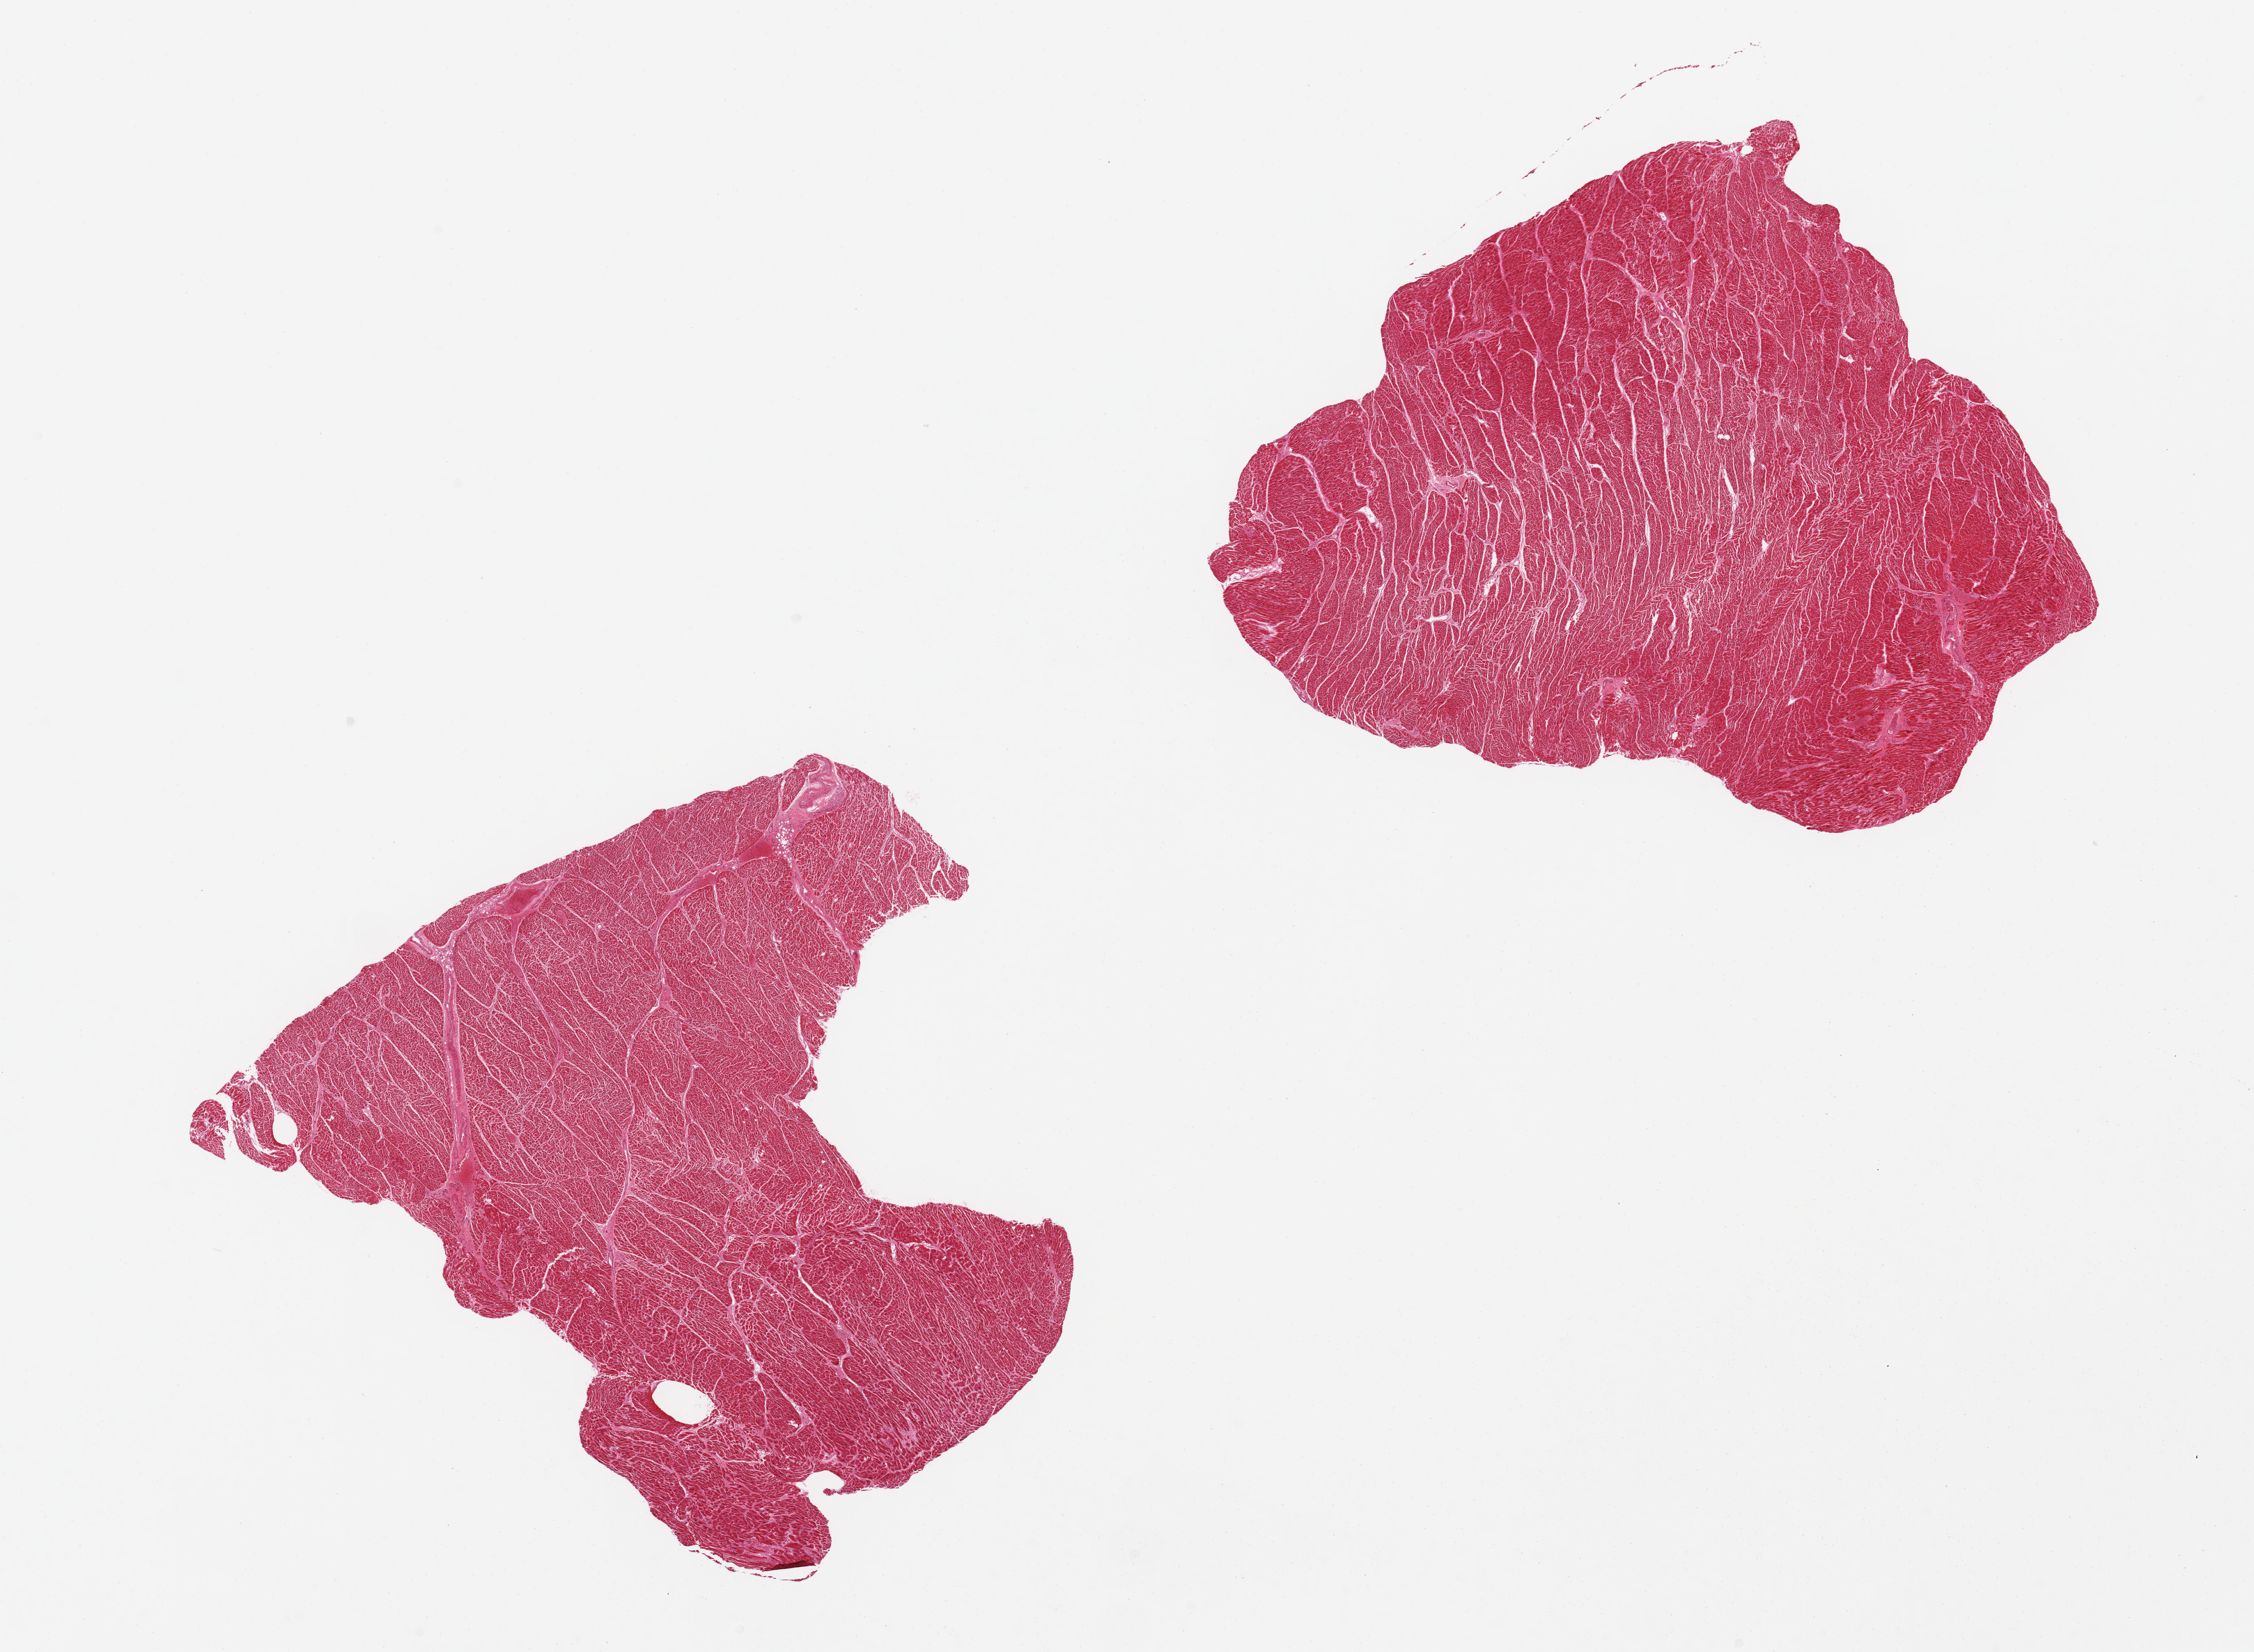
Whole-slide image, haematoxylin and eosin stain — low-resolution overview of the scanned area, about 25.6 x 18.8 mm; PAXgene-fixed paraffin-embedded (PFPE) section; sampled site (target tissue): heart; tissue donor sample. Donor: male.
Pathologist's review note for this sample: 2 pieces, mild interstitial fibrosis.